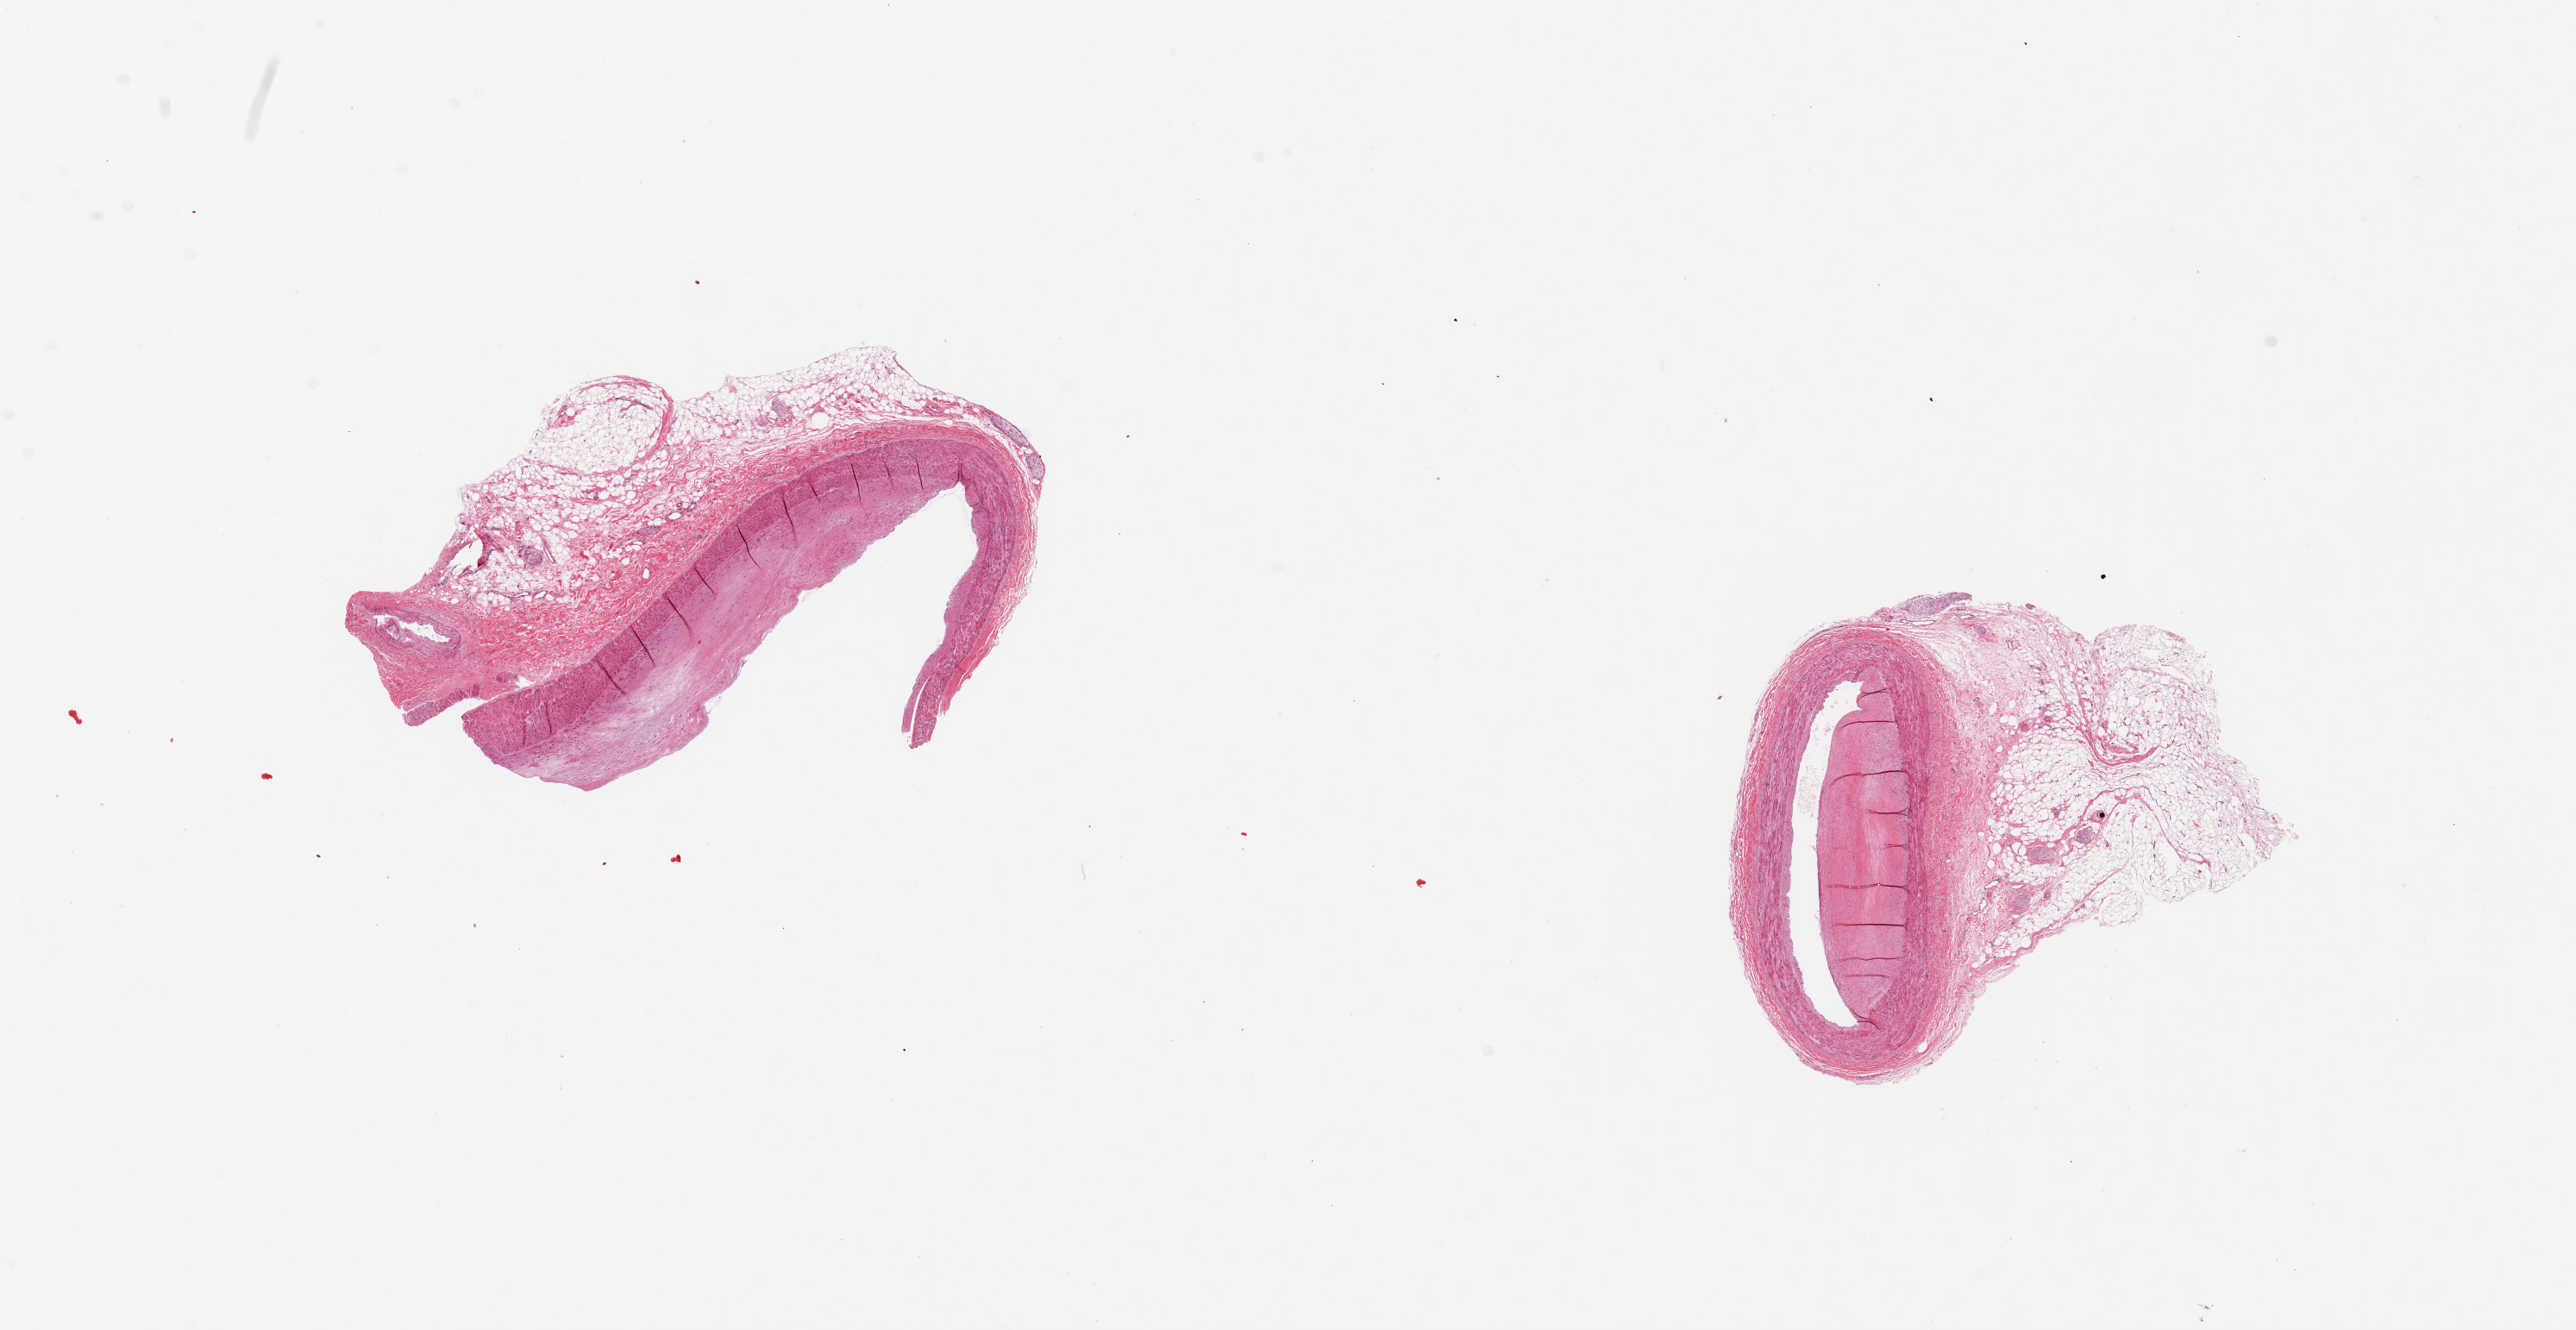
Digitized H&E-stained section — a low-resolution overview of the entire scanned area, about 23.6 x 12.2 mm (slide scanned at 20x); PAXgene-fixed, paraffin-embedded tissue; target tissue: coronary artery; donor tissue sample. Donor sex: female.
Reviewer comment on this tissue sample: 2 pieces, 6x3 & 5x4mm; up to 2mm adherent fat on both, arteries.